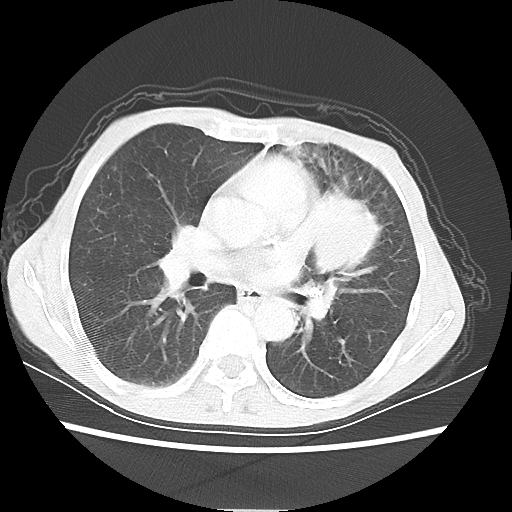
Chest CT, one axial slice; slice 32 of 56 in the series (ordered by position); reconstruction kernel LUNG; lung window (W 1500 / L -600 HU); 5 mm slice thickness; 512 × 512 image matrix, field of view 331 × 331 mm. Female patient, age 60 years. From the clinical record (not read from this slice): clinical TNM (as recorded): T4 N1 M0.
Outlined on this slice (bounding box drawn by a radiologist):
- lung tumour (recorded histology: adenocarcinoma): bounding box (x1, y1, x2, y2) in pixels: (310, 175, 385, 286)